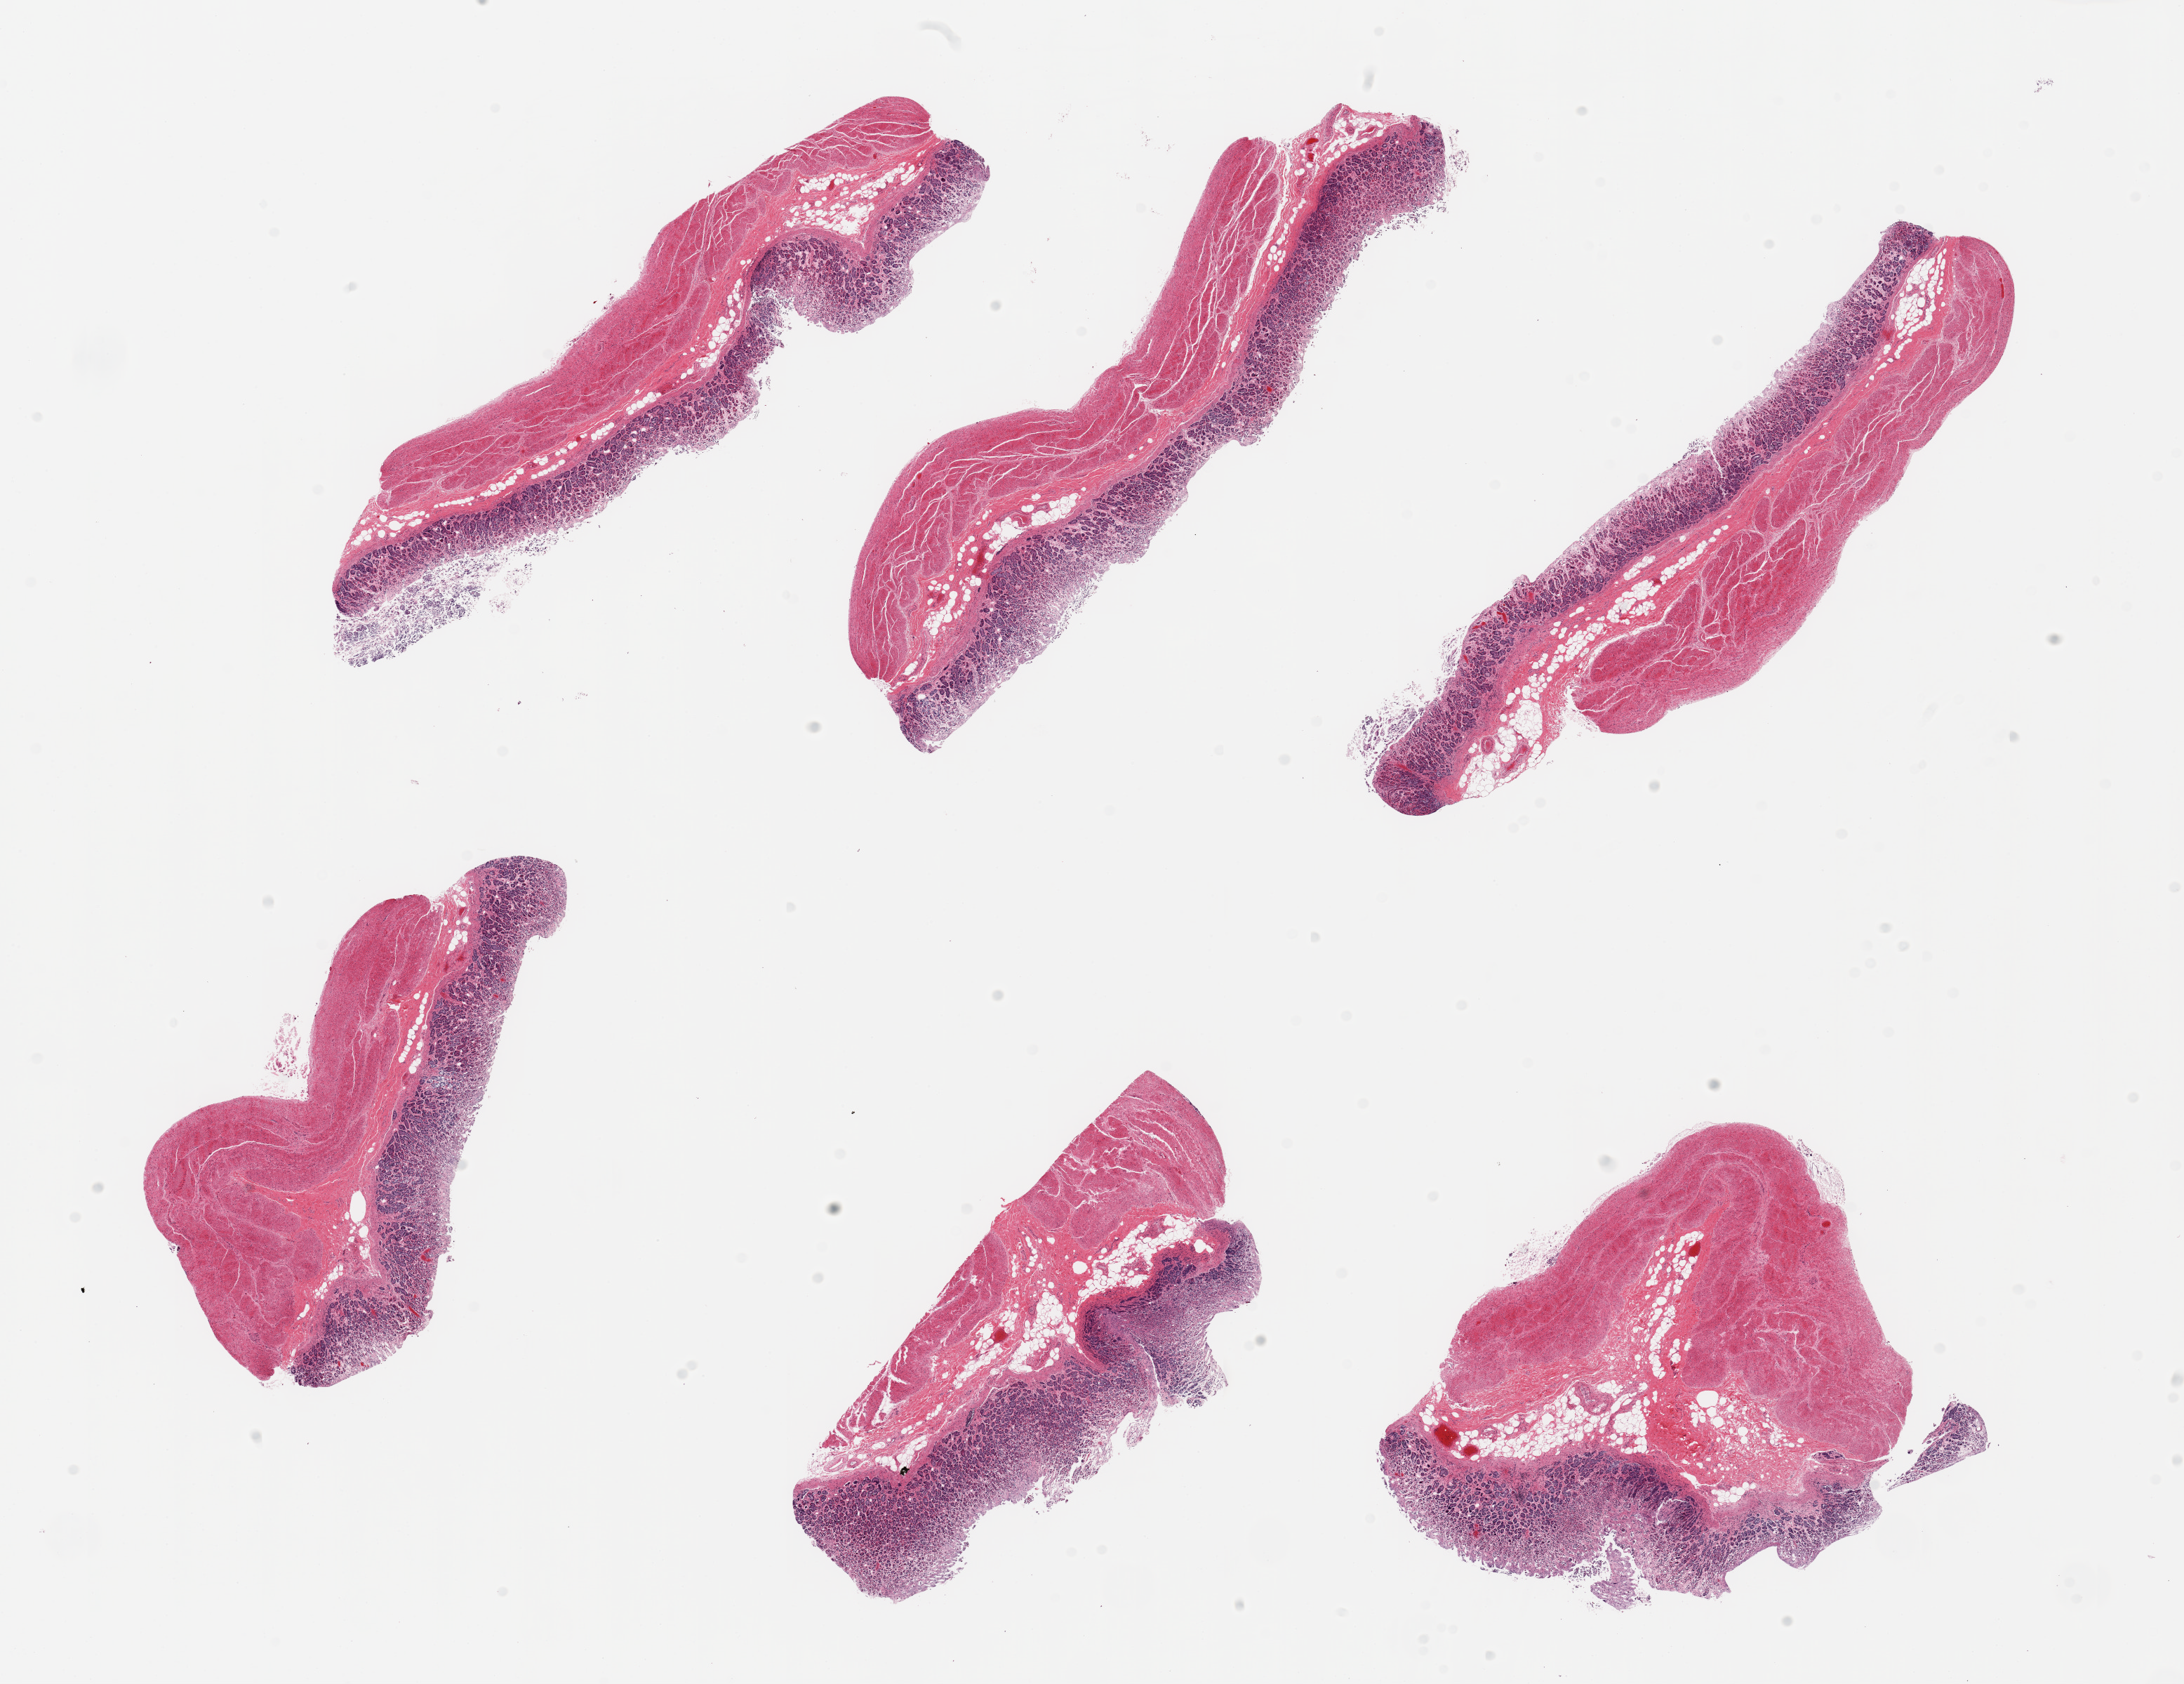
Haematoxylin and eosin whole-slide image, brightfield, low-resolution overview of the scanned area, about 24.6 x 19.0 mm; PAXgene-fixed, paraffin-embedded tissue; target tissue: stomach; donor tissue sample. Male donor.
Review note (as recorded): 6 pieces, mucosa moderate autolyzed, up to ~0.6mm, ~30% thickness.